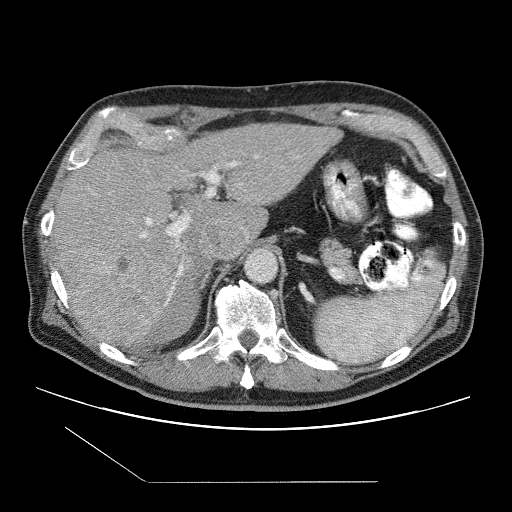
Contrast-enhanced abdominal CT (liver protocol), one axial slice; slice 67 of 109 in the series (ordered by position); reconstruction kernel STANDARD; one of 2 acquisitions stored at this slice position; soft-tissue window (W 400 / L 40 HU); 512 × 512 image matrix. From the clinical record (not read from this slice): diagnosis: hepatocellular carcinoma (patient treated with transarterial chemoembolisation; whether this scan precedes or follows treatment is not stated here); TNM stage (as recorded): Stage-IIIB; Child-Pugh class: A; tumour differentiation: well differentiated.
Structures marked on this image (semi-automatic segmentation, software-assisted and operator-edited):
- abdominal aorta: bounding box [x1, y1, x2, y2] px = [245, 249, 279, 283]
- liver parenchyma outside the tumour (the mass and vessels are separate outlines, so this box may not span the whole liver): [52, 124, 340, 346]
- mass: [58, 241, 176, 337]
- liver vessels: [140, 156, 258, 304]